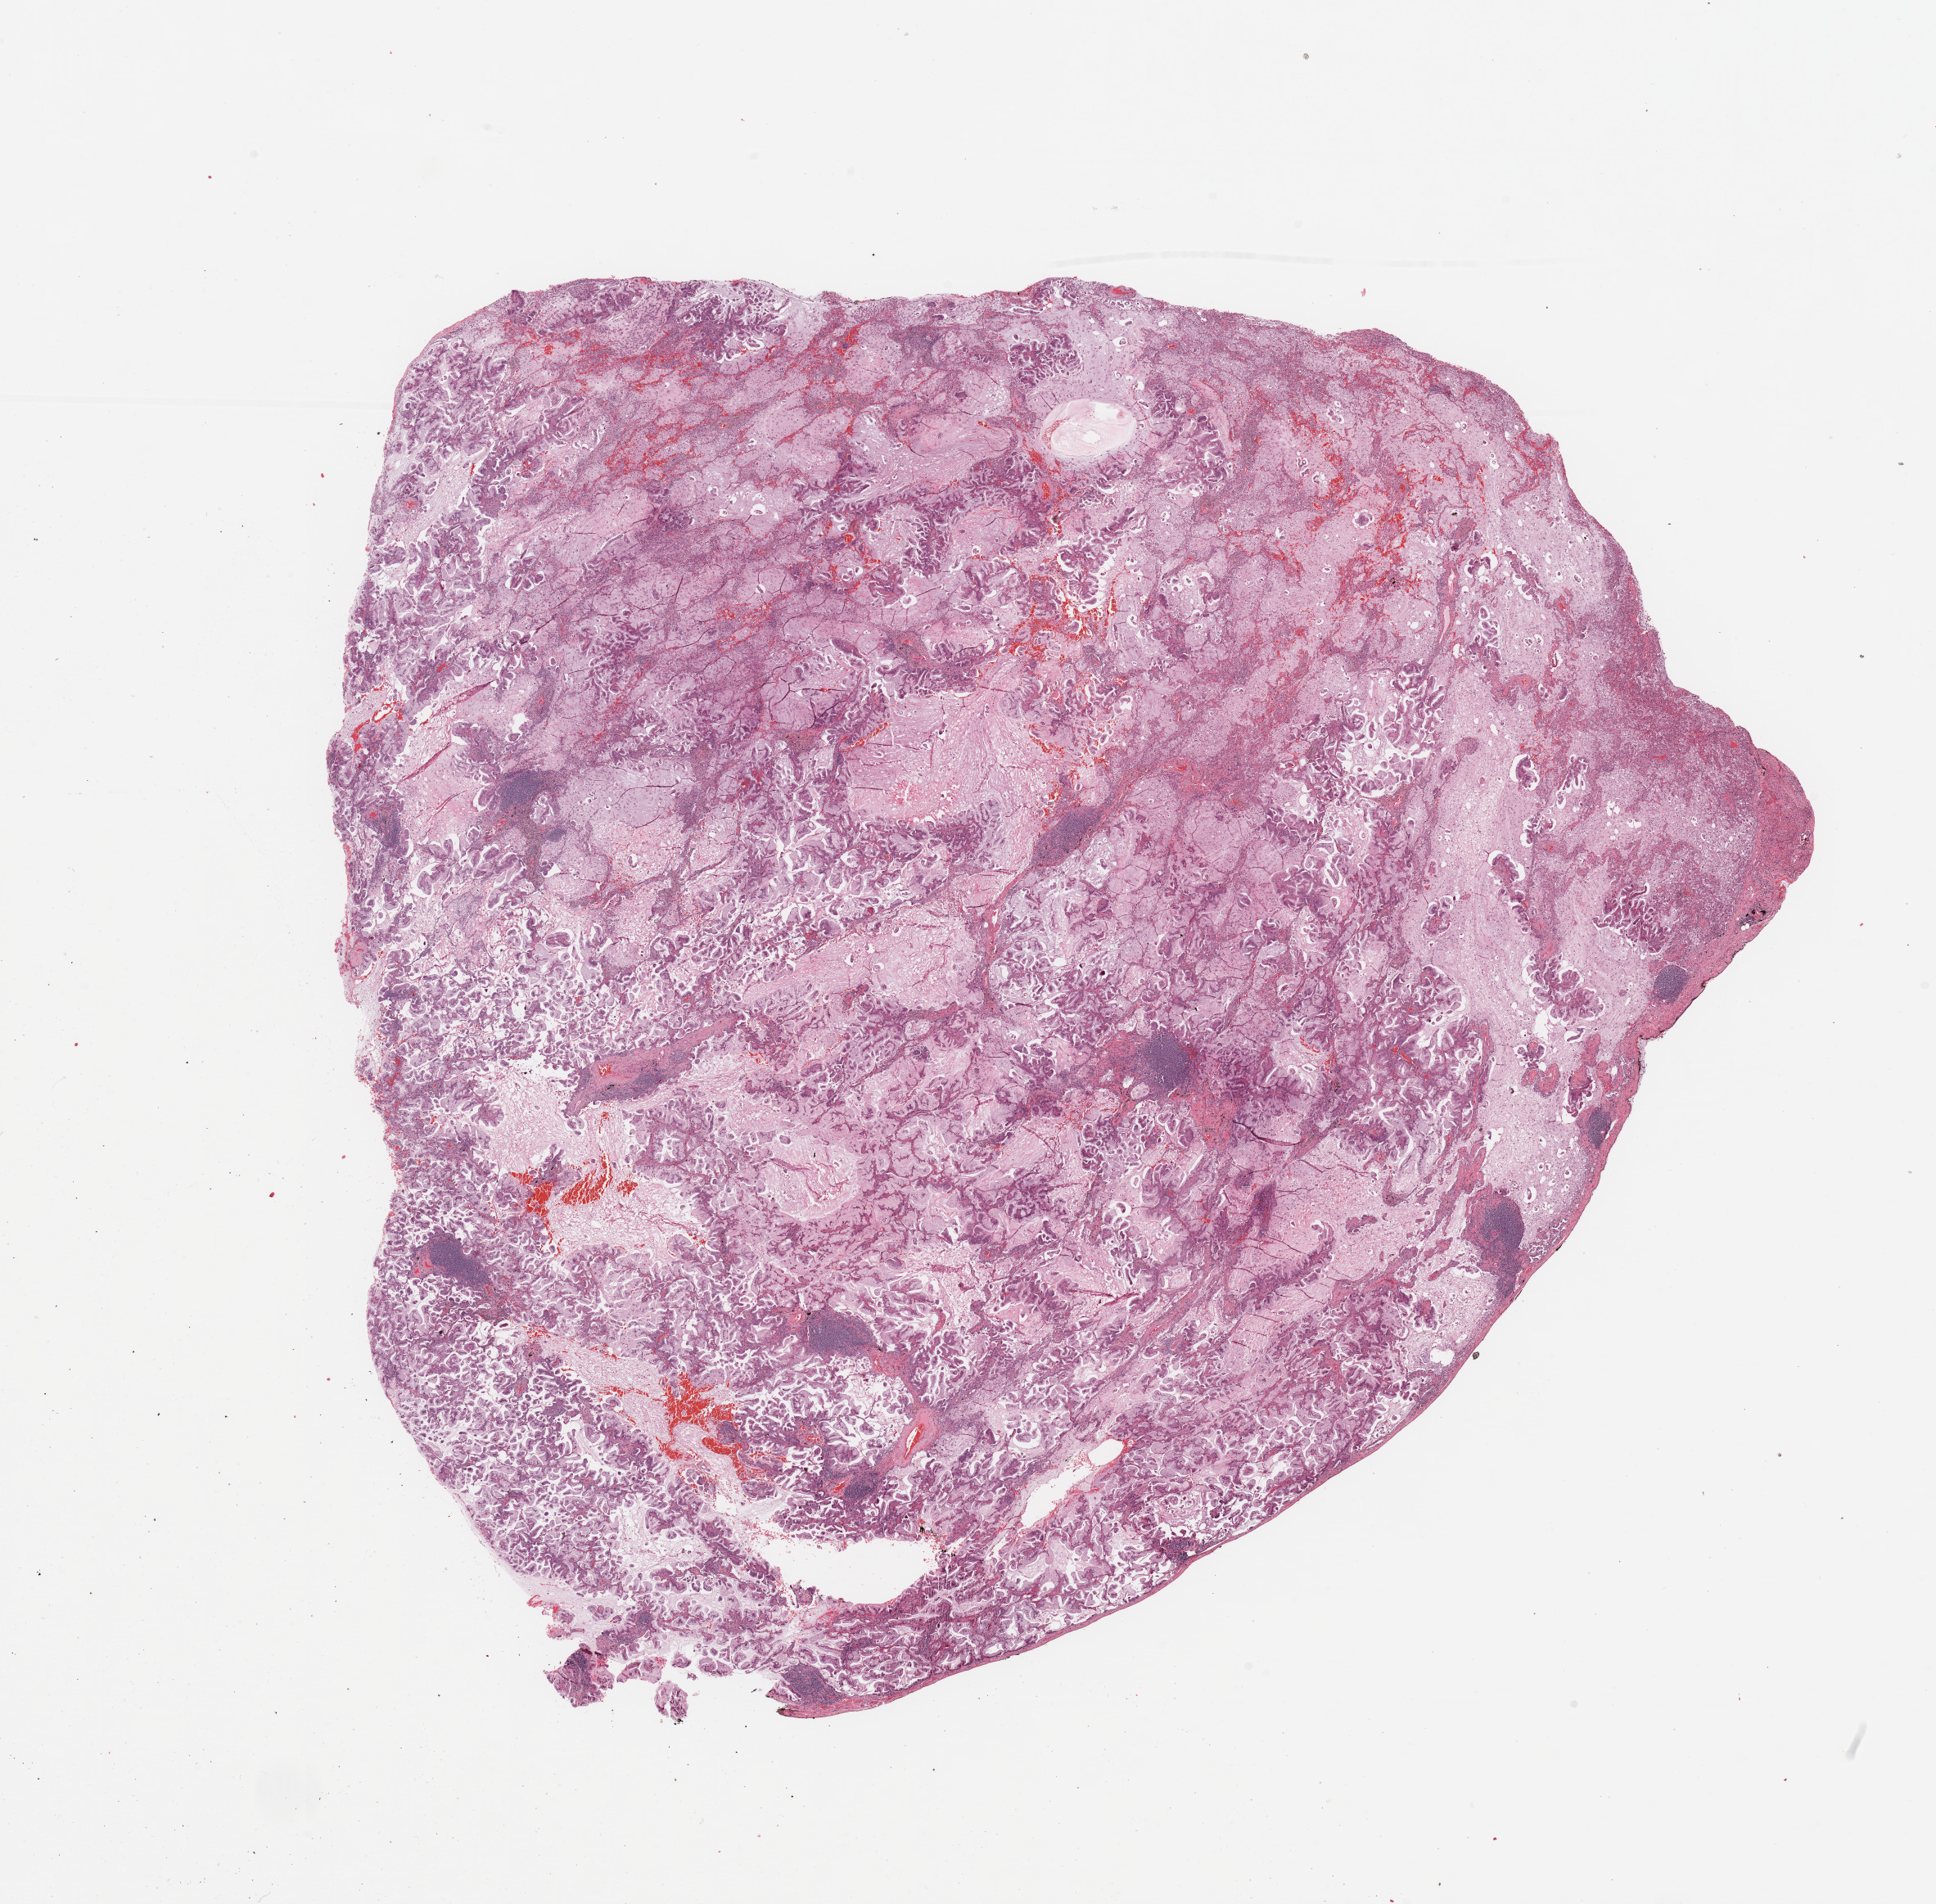
Whole-slide histology image, Hematoxylin and eosin (H&E) stained, low-resolution overview of the scanned area, about 18.7 x 18.4 mm; tumour tissue sample, sampled site: lung. Patient: male, age 71 years. Histologic grade: G2 (moderately differentiated). Composition of this section per pathologist review: tumour nuclei 80%, necrosis 0%.
AJCC pathologic stage: IA. Histologic diagnosis: Adenocarcinoma, NOS.